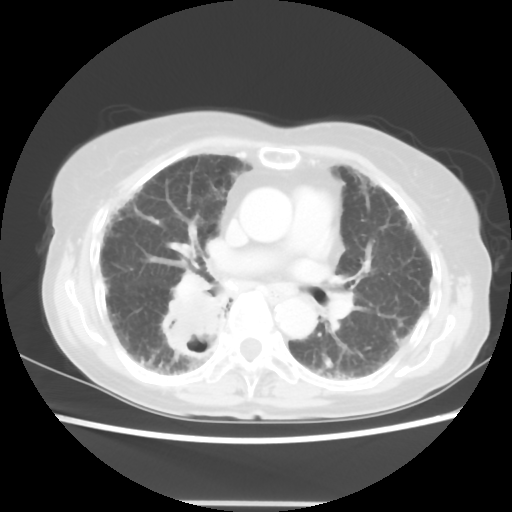
Chest CT, one axial slice. Position 29 of 52 along the scan axis. Reconstruction kernel STANDARD. 120 kVp. Lung window (W 1500 / L -600 HU). 5 mm slice thickness. 512 × 512 image matrix. Female patient, age 71 years. From the clinical record (not read from this slice): clinical TNM (as recorded): T3 N0 M0.
Structures marked on this image (rectangle marked by the reading radiologist):
- lung tumour (recorded histology: squamous cell carcinoma): bounding box <152,286,236,371> (left, top, right, bottom; pixels)